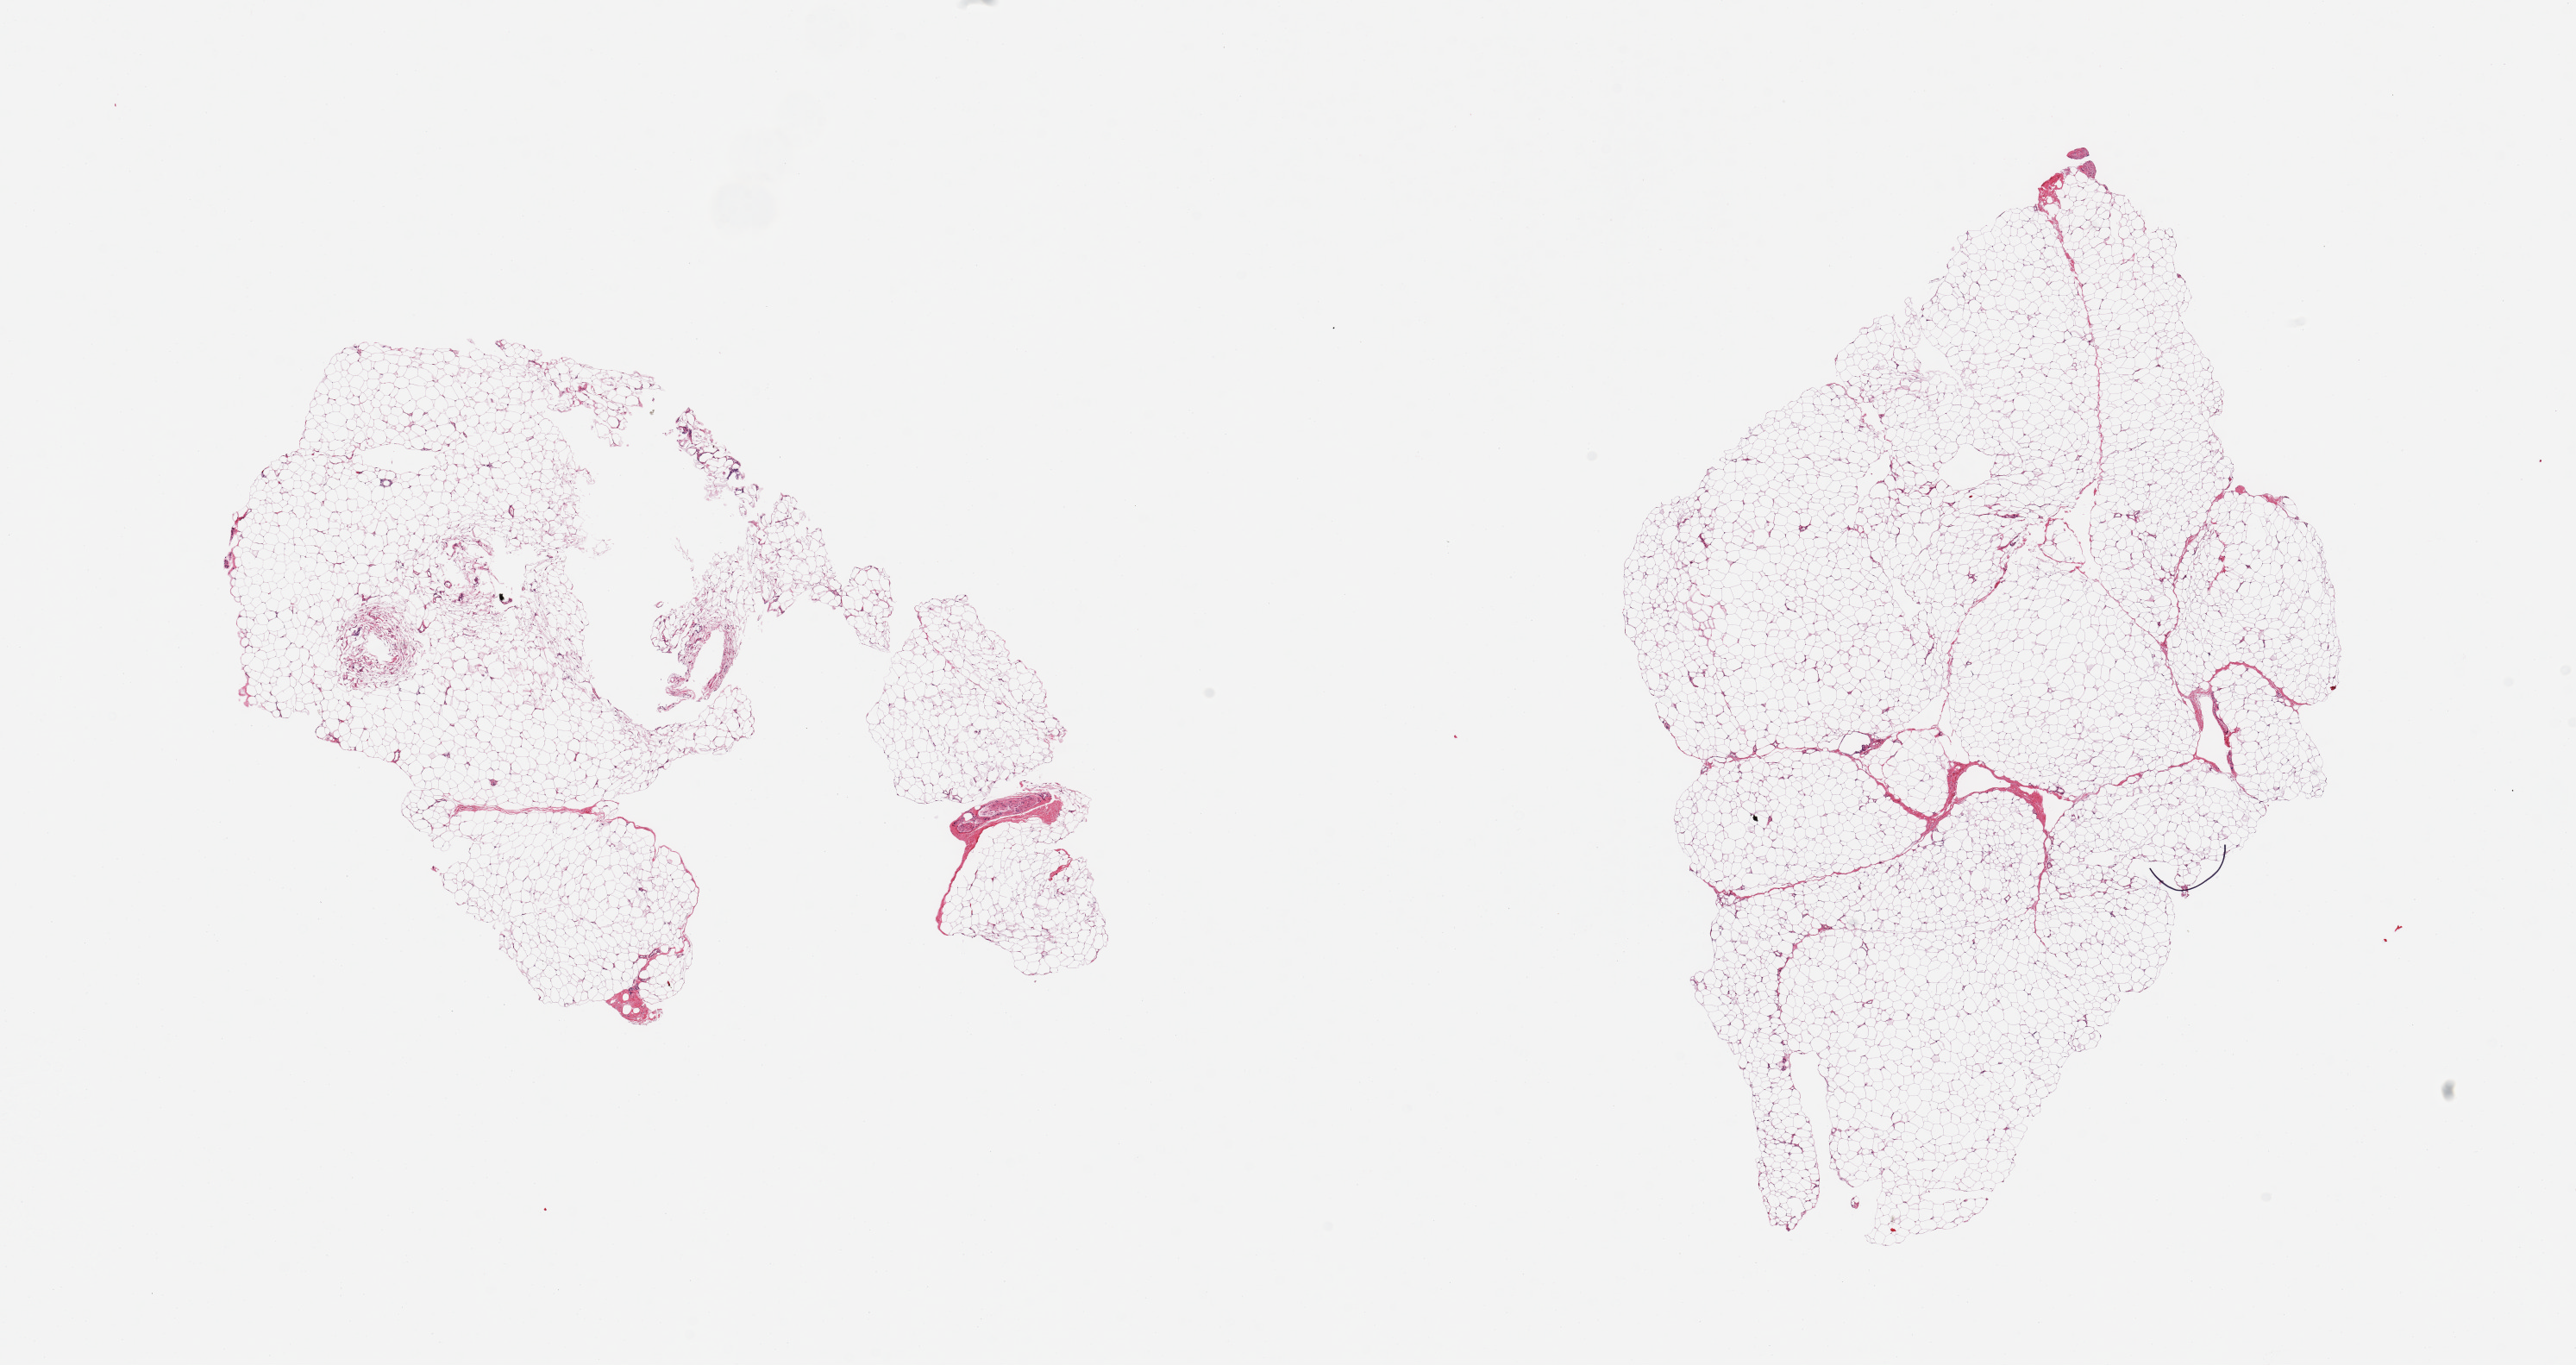
Haematoxylin and eosin whole-slide image, whole scanned area (about 23.6 x 12.5 mm, from a 20x scan) shown as a low-resolution overview; PAXgene-fixed, paraffin-embedded tissue; section of adipose tissue (target tissue); donor tissue sample.
Pathologist's review note for this sample: 2 pieces; <5% fibrous content.